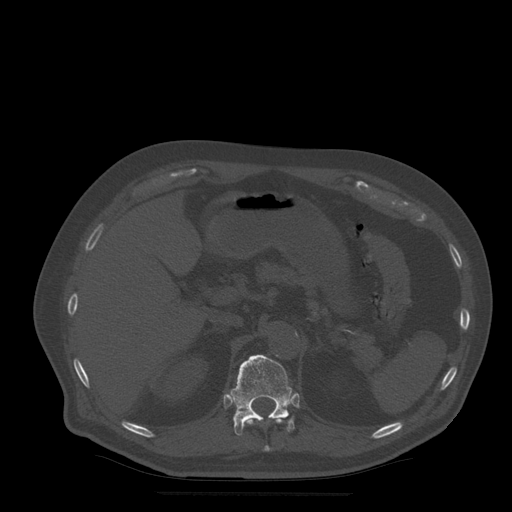
CT including the spine, one axial slice. Slice 227 of 522 in the series (ordered by position). Bone window (W 1800 / L 400 HU). 512 × 512 image matrix, field of view 420 × 420 mm. Patient age 72 years. From the clinical record (not read from this slice): primary cancer: prostate.
Outlined on this slice (semi-automatically segmented with operator editing):
- T11 vertebra: box from (x=248, y=417) to (x=284, y=452) px
- T12 vertebra: (x=231, y=355)–(x=295, y=436)